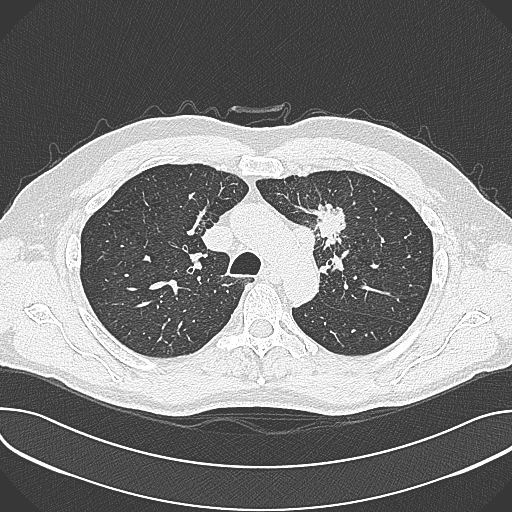
Low-dose screening chest CT, axial slice. Baseline annual screen. Lung window (W 1500 / L -600 HU). Slice 97 of 361 in the series. 512 × 512 image matrix. Male, age 59 years at enrolment. Current smoker at enrolment.
• Lesion marked by an expert reader, bounding box [x1, y1, x2, y2] px = [302, 198, 360, 257].
• The screening reader recorded 2 non-calcified nodules or masses ≥4 mm on this exam (left upper lobe, left upper lobe); which of them this box marks is not recorded.
• Later outcome: lung cancer diagnosed 21 days after this screen — non-small cell carcinoma, left upper lobe, poorly differentiated (G3), stage IIIA (AJCC 6th edition), 35 mm at pathology.